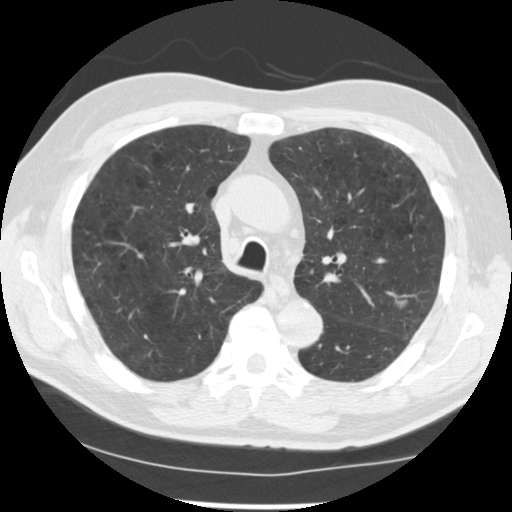
Low-dose screening chest CT, one axial slice. Lung window (W 1500 / L -600 HU). 2.5 mm slice thickness. 512 × 512 image matrix.
Outlined on this slice (manually delineated by an expert):
- lesion 1 (tumor, upper lobe of left lung): box from (x=399, y=301) to (x=405, y=305) px